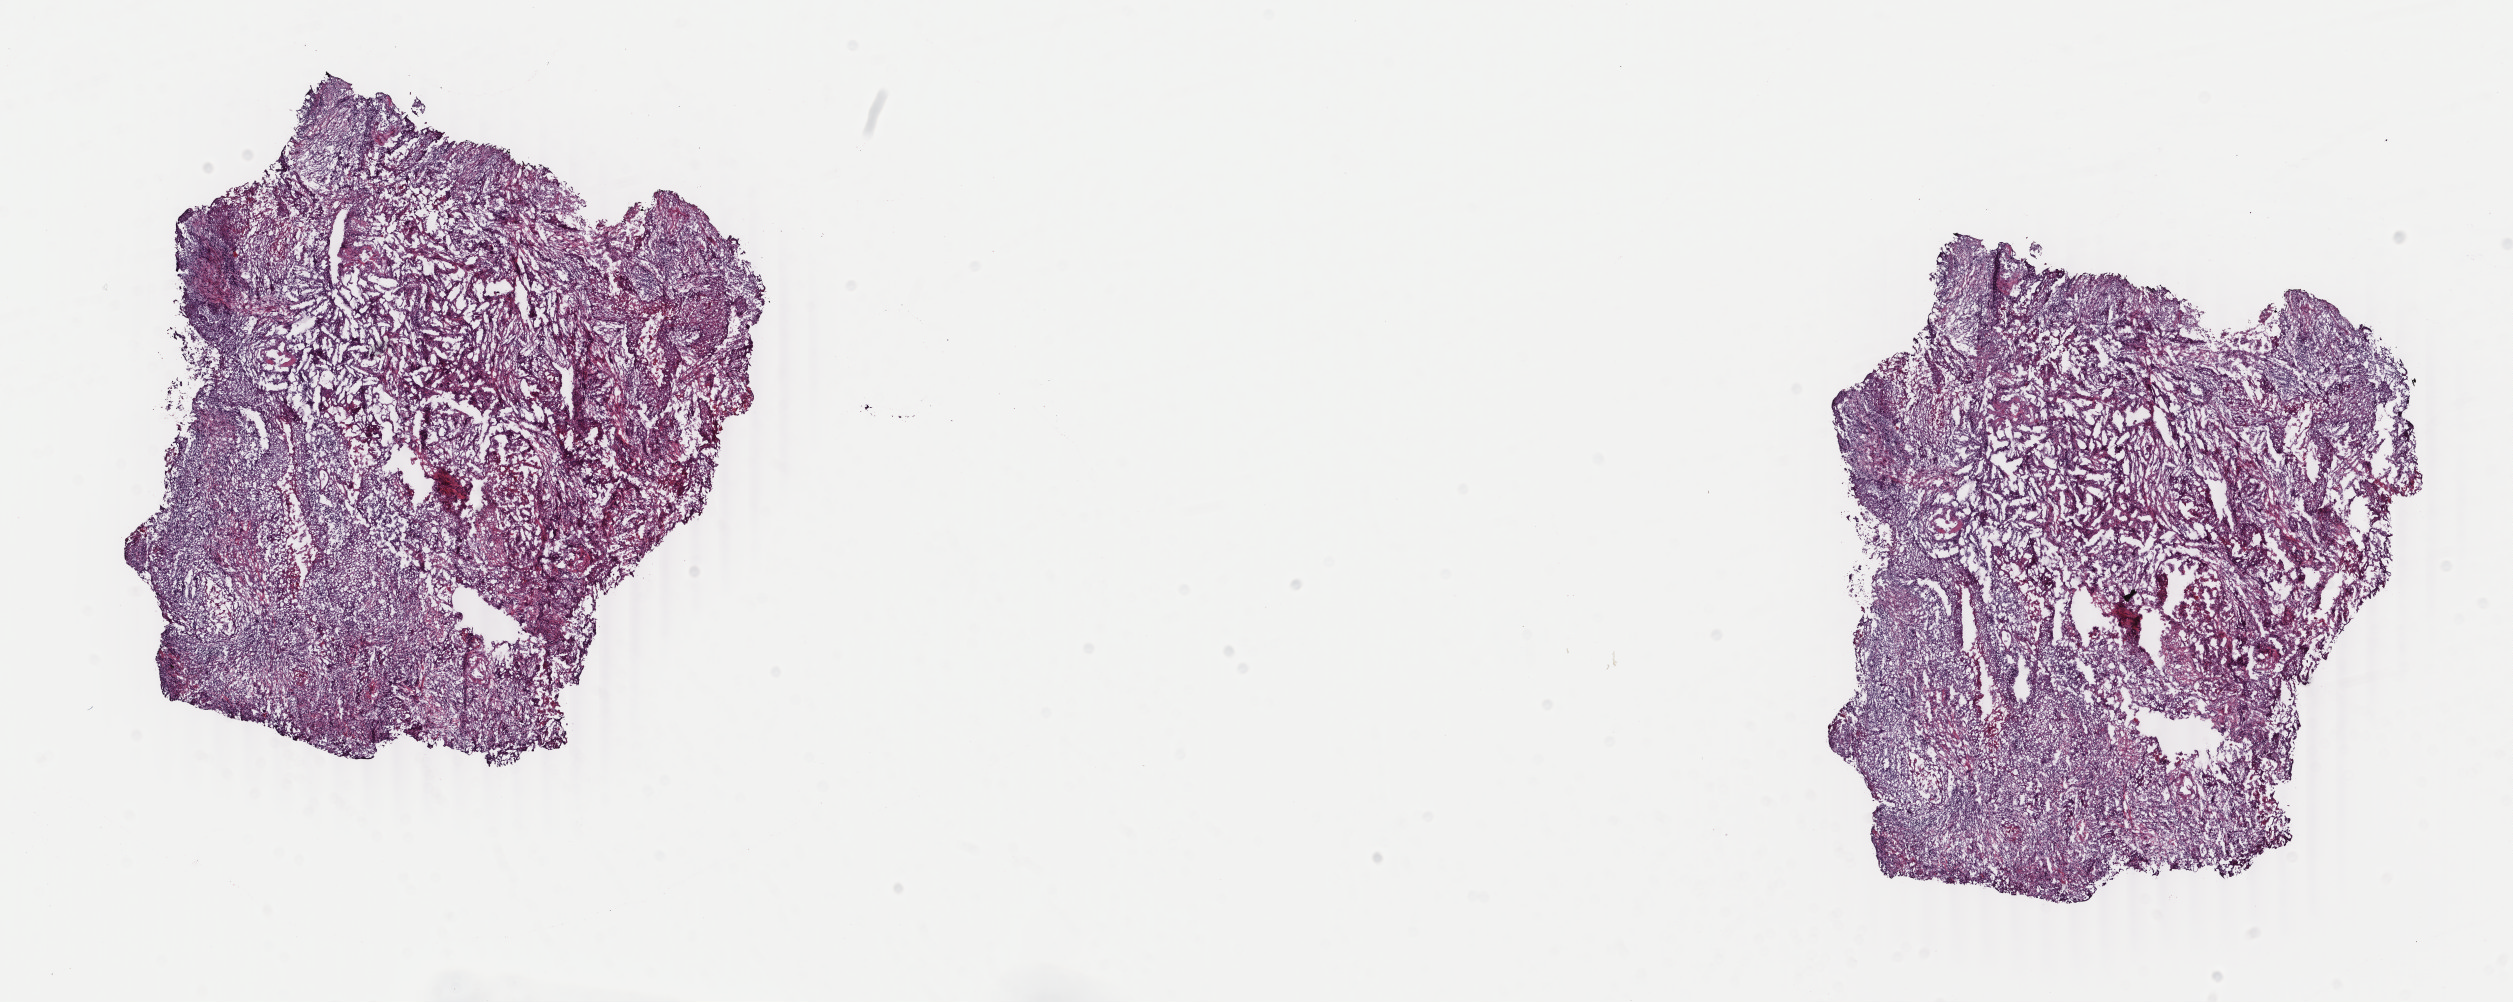
Digitized H&E tissue section (whole slide) — whole scanned area (about 20.0 x 8.0 mm, from a 40x scan) shown as a low-resolution overview, frozen section from the top of the tissue portion, primary tumour sample from the lung. Male patient.
Histologic diagnosis: Squamous cell carcinoma, keratinizing, NOS (upper lobe, lung).